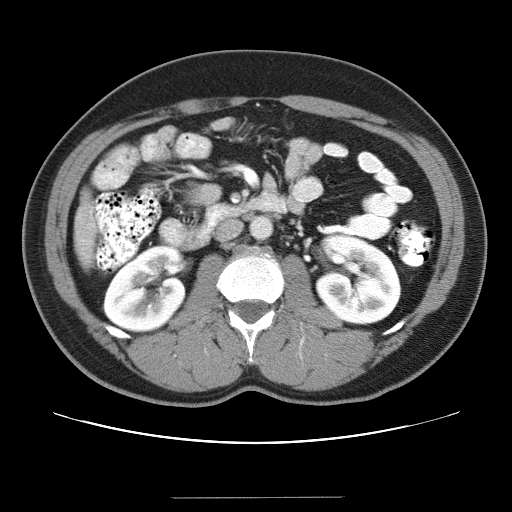
Contrast-enhanced abdominal CT (liver protocol), one axial slice. Slice 5 of 40 in the series (ordered by position). Reconstruction kernel STANDARD. Soft-tissue window (W 400 / L 40 HU). 512 × 512 image matrix. From the clinical record (not read from this slice): diagnosis: hepatocellular carcinoma (patient treated with transarterial chemoembolisation; whether this scan precedes or follows treatment is not stated here); TNM stage (as recorded): Stage-IVA; Child-Pugh class: B.
Annotated regions visible in this slice (semi-automatic segmentation, software-assisted and operator-edited):
- liver parenchyma outside the tumour (the mass and vessels are separate outlines, so this box may not span the whole liver): bounding box <74,192,96,263> (left, top, right, bottom; pixels)